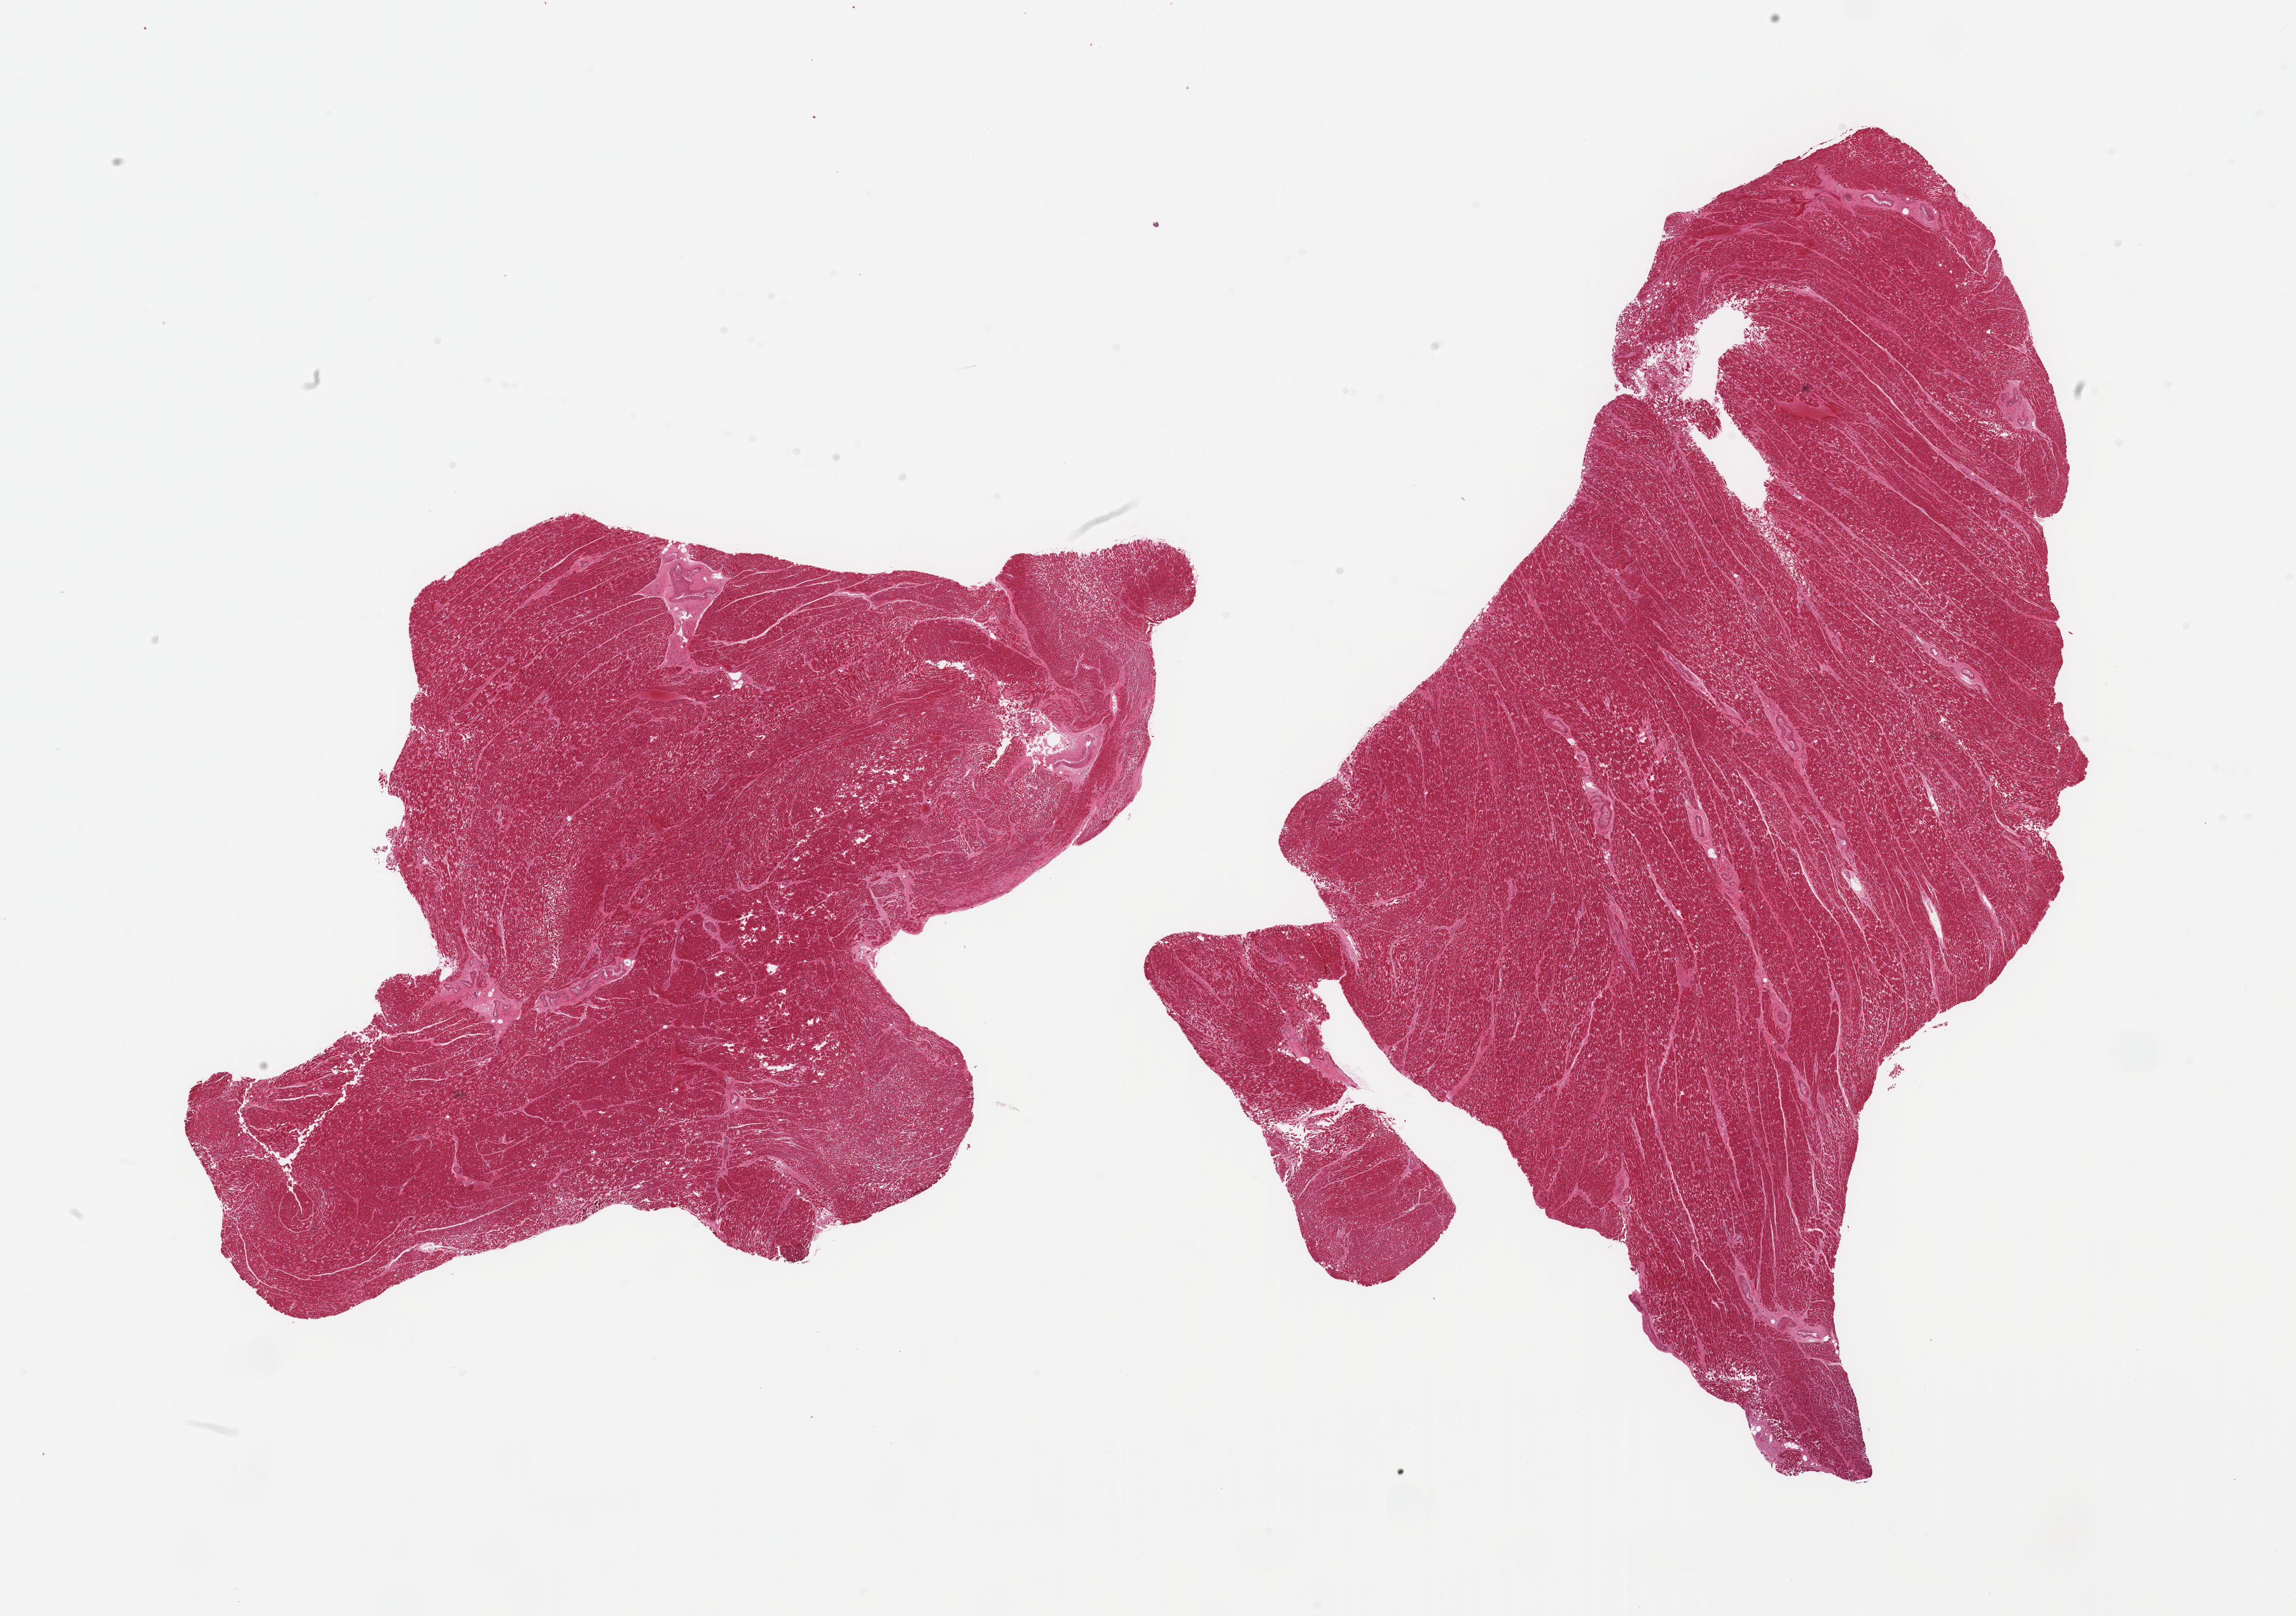
Digitized haematoxylin and eosin-stained section, low-resolution overview of the scanned area, about 28.5 x 20.1 mm (acquisition: 20x scan), PAXgene-fixed, paraffin-embedded tissue, sampled site (target tissue): heart, donor tissue sample. Donor: male.
Review note (as recorded): 2 pieces, moderate interstitial fibrosis/chronic ischemic changes.